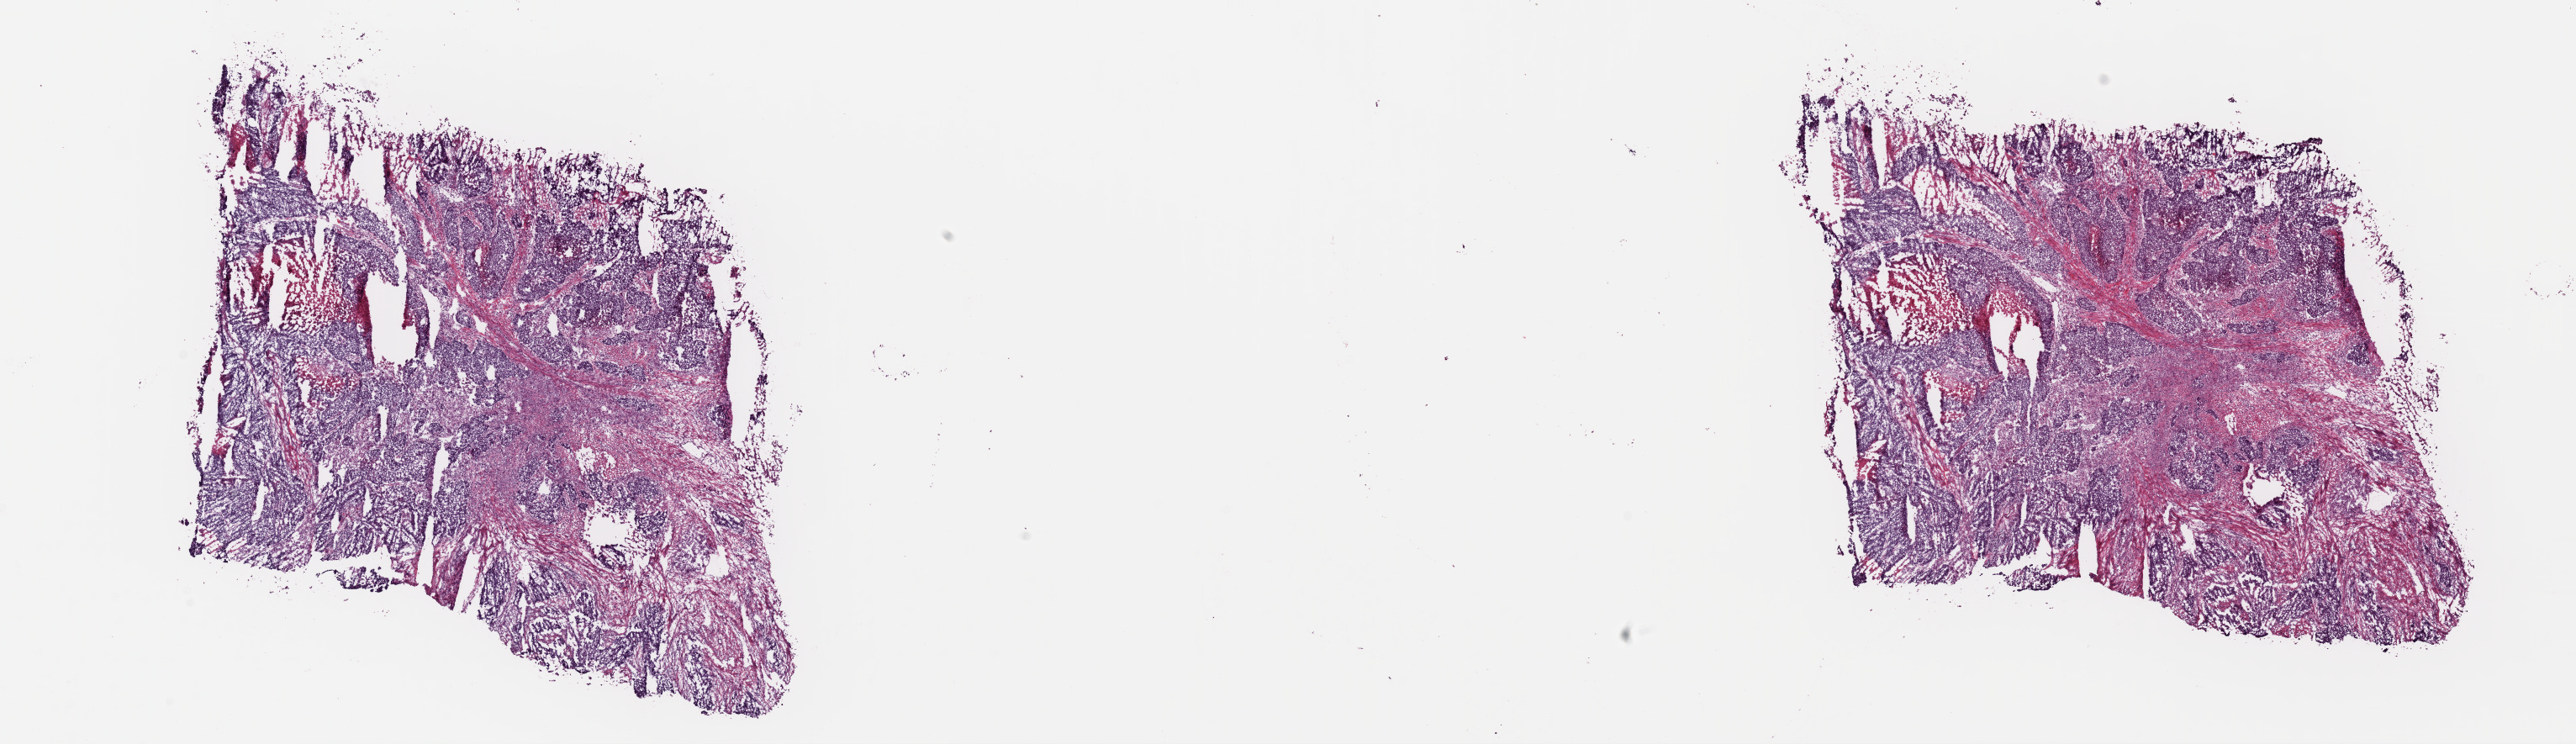
Digitized H&E tissue section (whole slide), whole scanned area (about 24.2 x 7.0 mm) shown as a low-resolution overview, frozen section from the top of the tissue portion, sample: primary tumour, uterus. Patient: female, age at initial diagnosis 43 years. Histologic grade: G3 (poorly differentiated). Slide review estimates, as recorded: tumour cells 70%, tumour nuclei 70%, normal cells 0%, stromal cells 20%, necrosis 10%. Infiltration values recorded for this section: lymphocyte infiltration 0%, monocyte infiltration 0%, neutrophil infiltration 0%.
Diagnosis: Endometrioid adenocarcinoma, NOS (endometrium). FIGO stage: IIIC2.